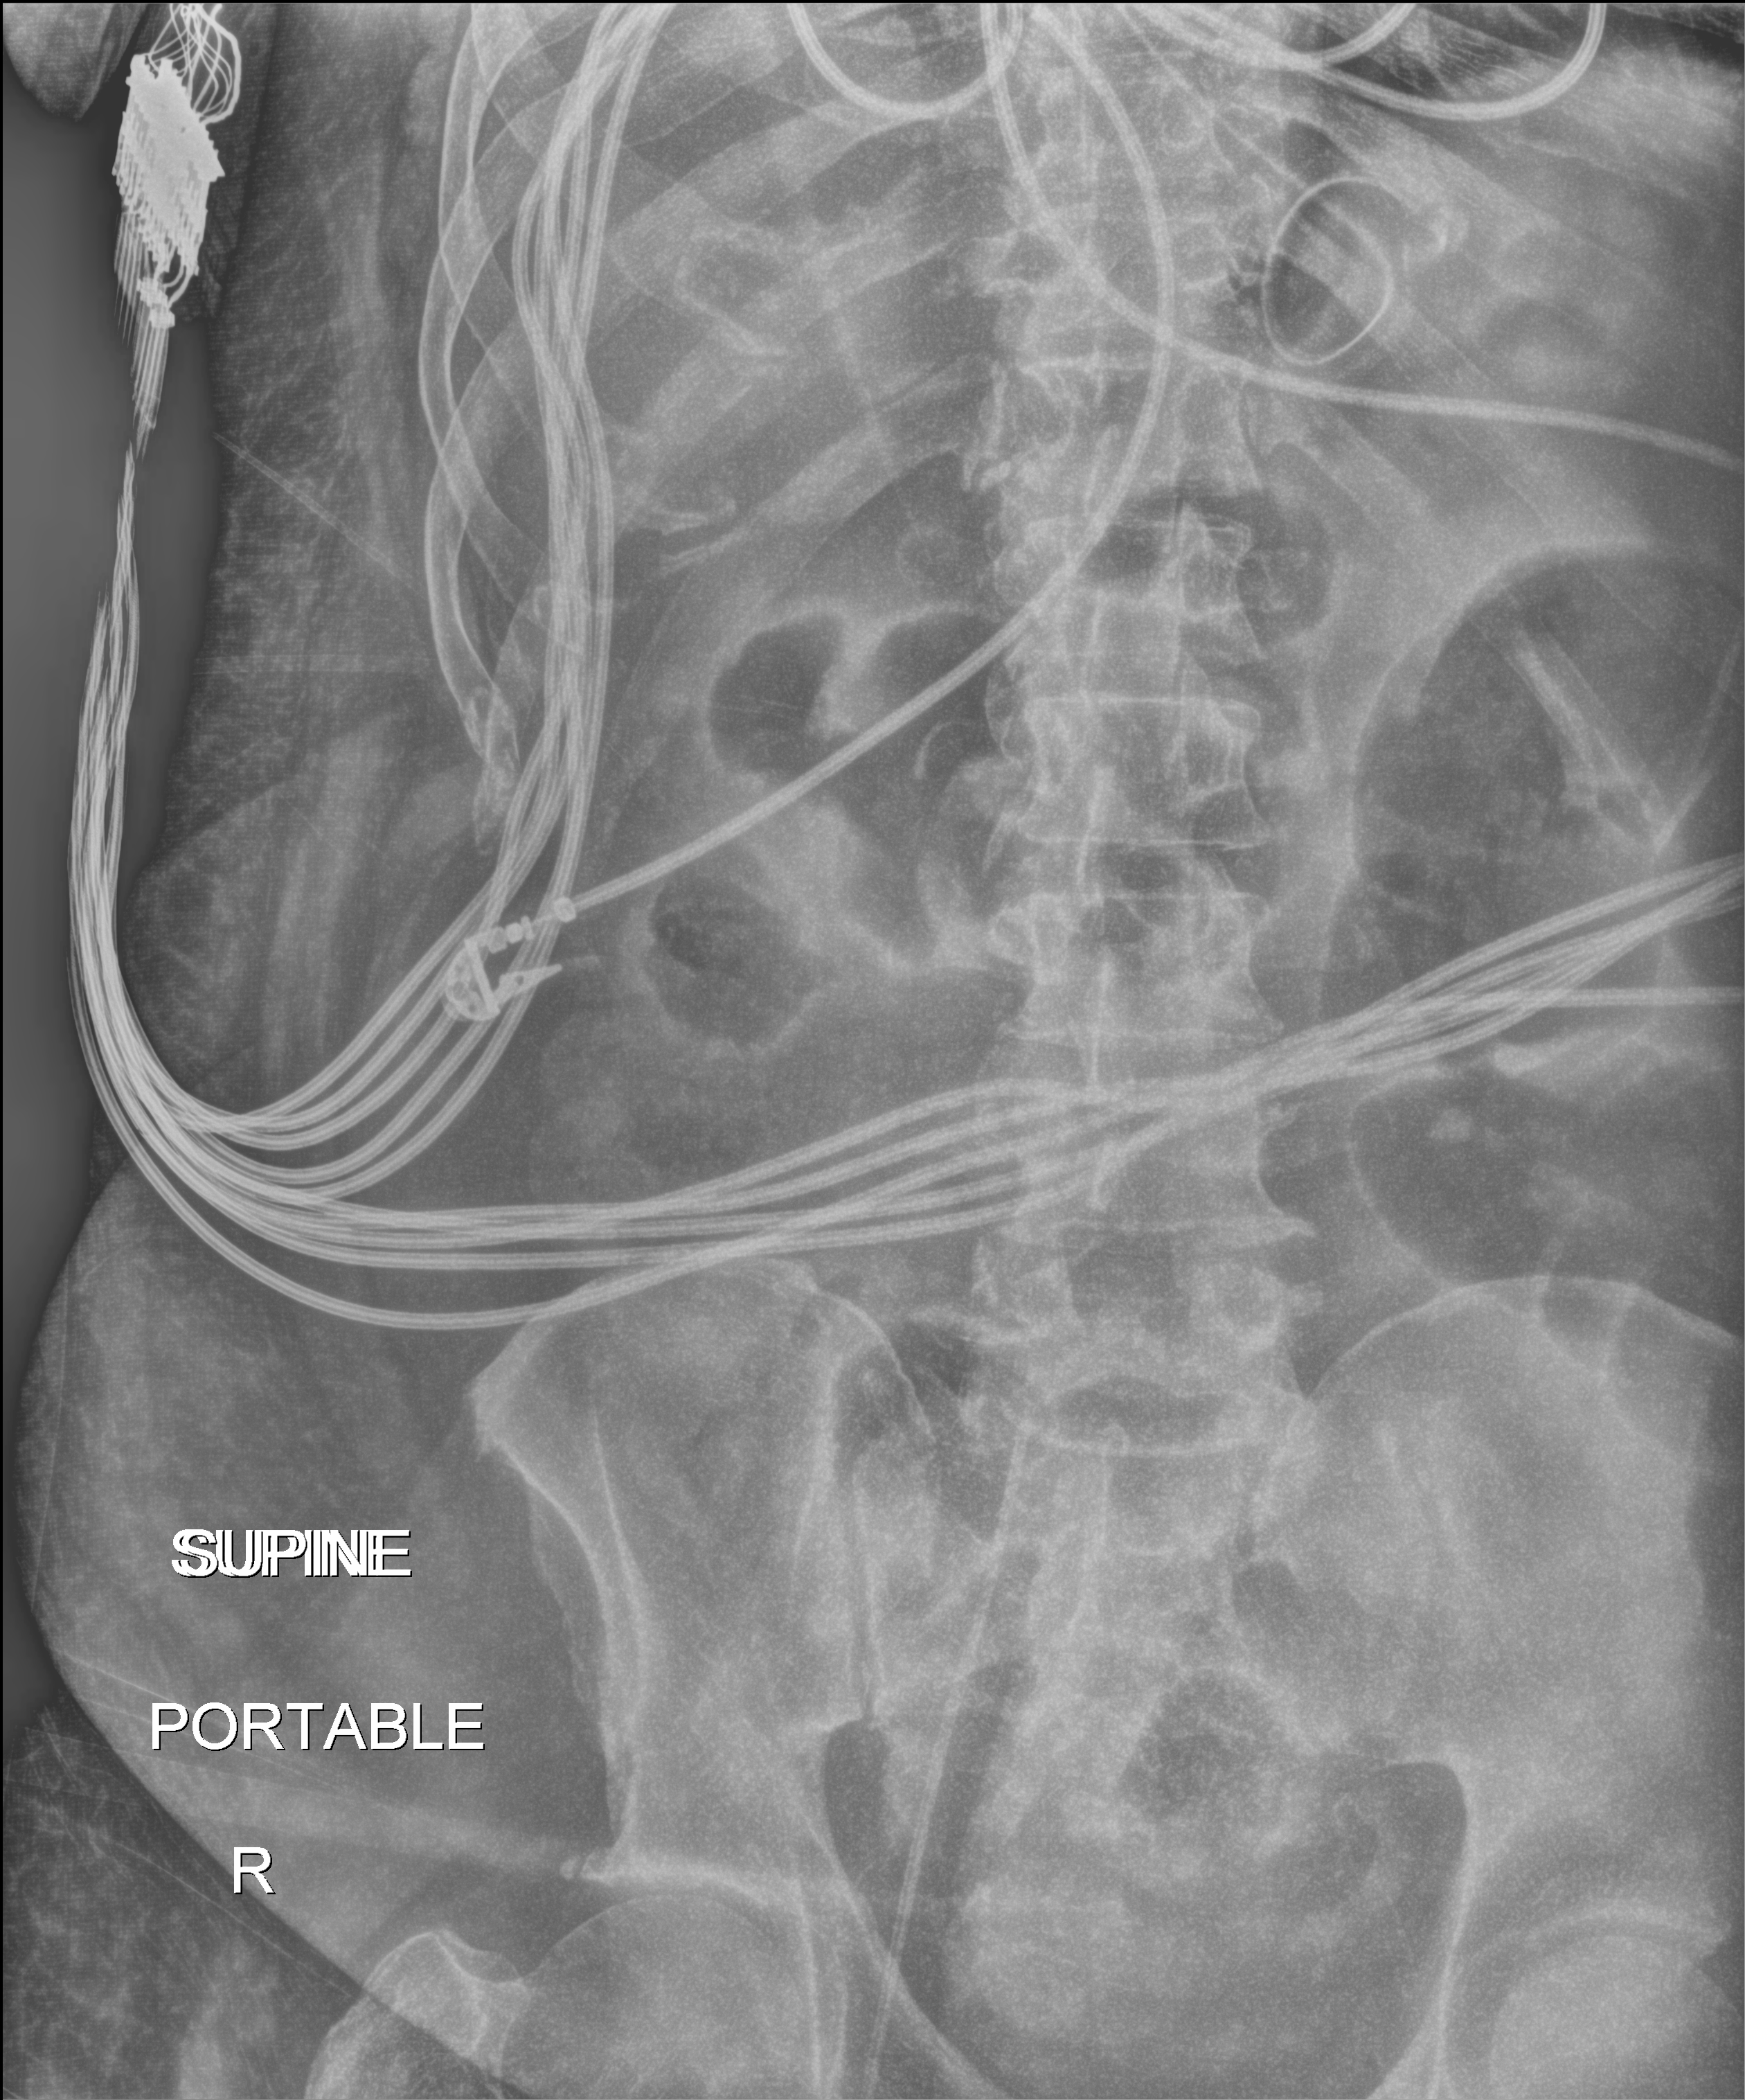
Bedside abdomen radiograph (digital radiography), anteroposterior (AP) projection. Patient hospitalised with COVID-19, aged 18–59 years.
Admission-level facts for this patient (not findings on this image; timing relative to this image not recorded):
- other chronic lung disease (admission record): no
- COPD (admission record): no